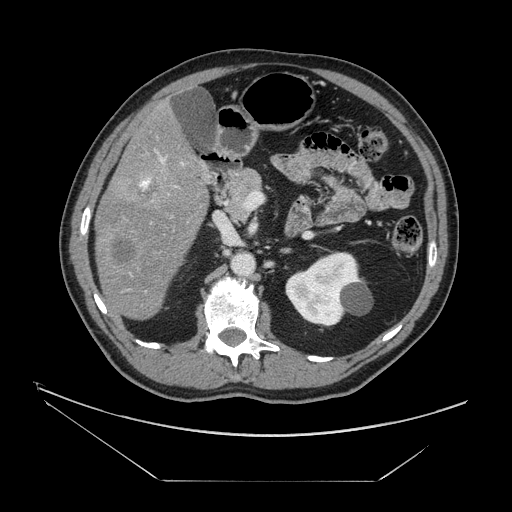
Contrast-enhanced abdominal CT, one axial slice; slice 73 of 161 in the series (ordered by position); 120 kVp; intravenous contrast given; soft-tissue window (W 400 / L 40 HU); 2.5 mm slice thickness; 512 × 512 image matrix. Male patient, age 65 years. From the clinical record (not read from this slice): diagnosis: colorectal cancer liver metastases, imaged before liver resection; multiple liver metastases: yes; largest metastasis: 4.2 cm; chemotherapy before resection: yes.
Annotated regions visible in this slice (outlined manually by an expert reader):
- liver: bounding box (x1, y1, x2, y2) in pixels: (96, 108, 208, 319)
- portal vein (with intrahepatic branches): (141, 157, 176, 188)
- liver metastasis: (114, 240, 138, 266)
- liver metastasis: (130, 176, 161, 199)